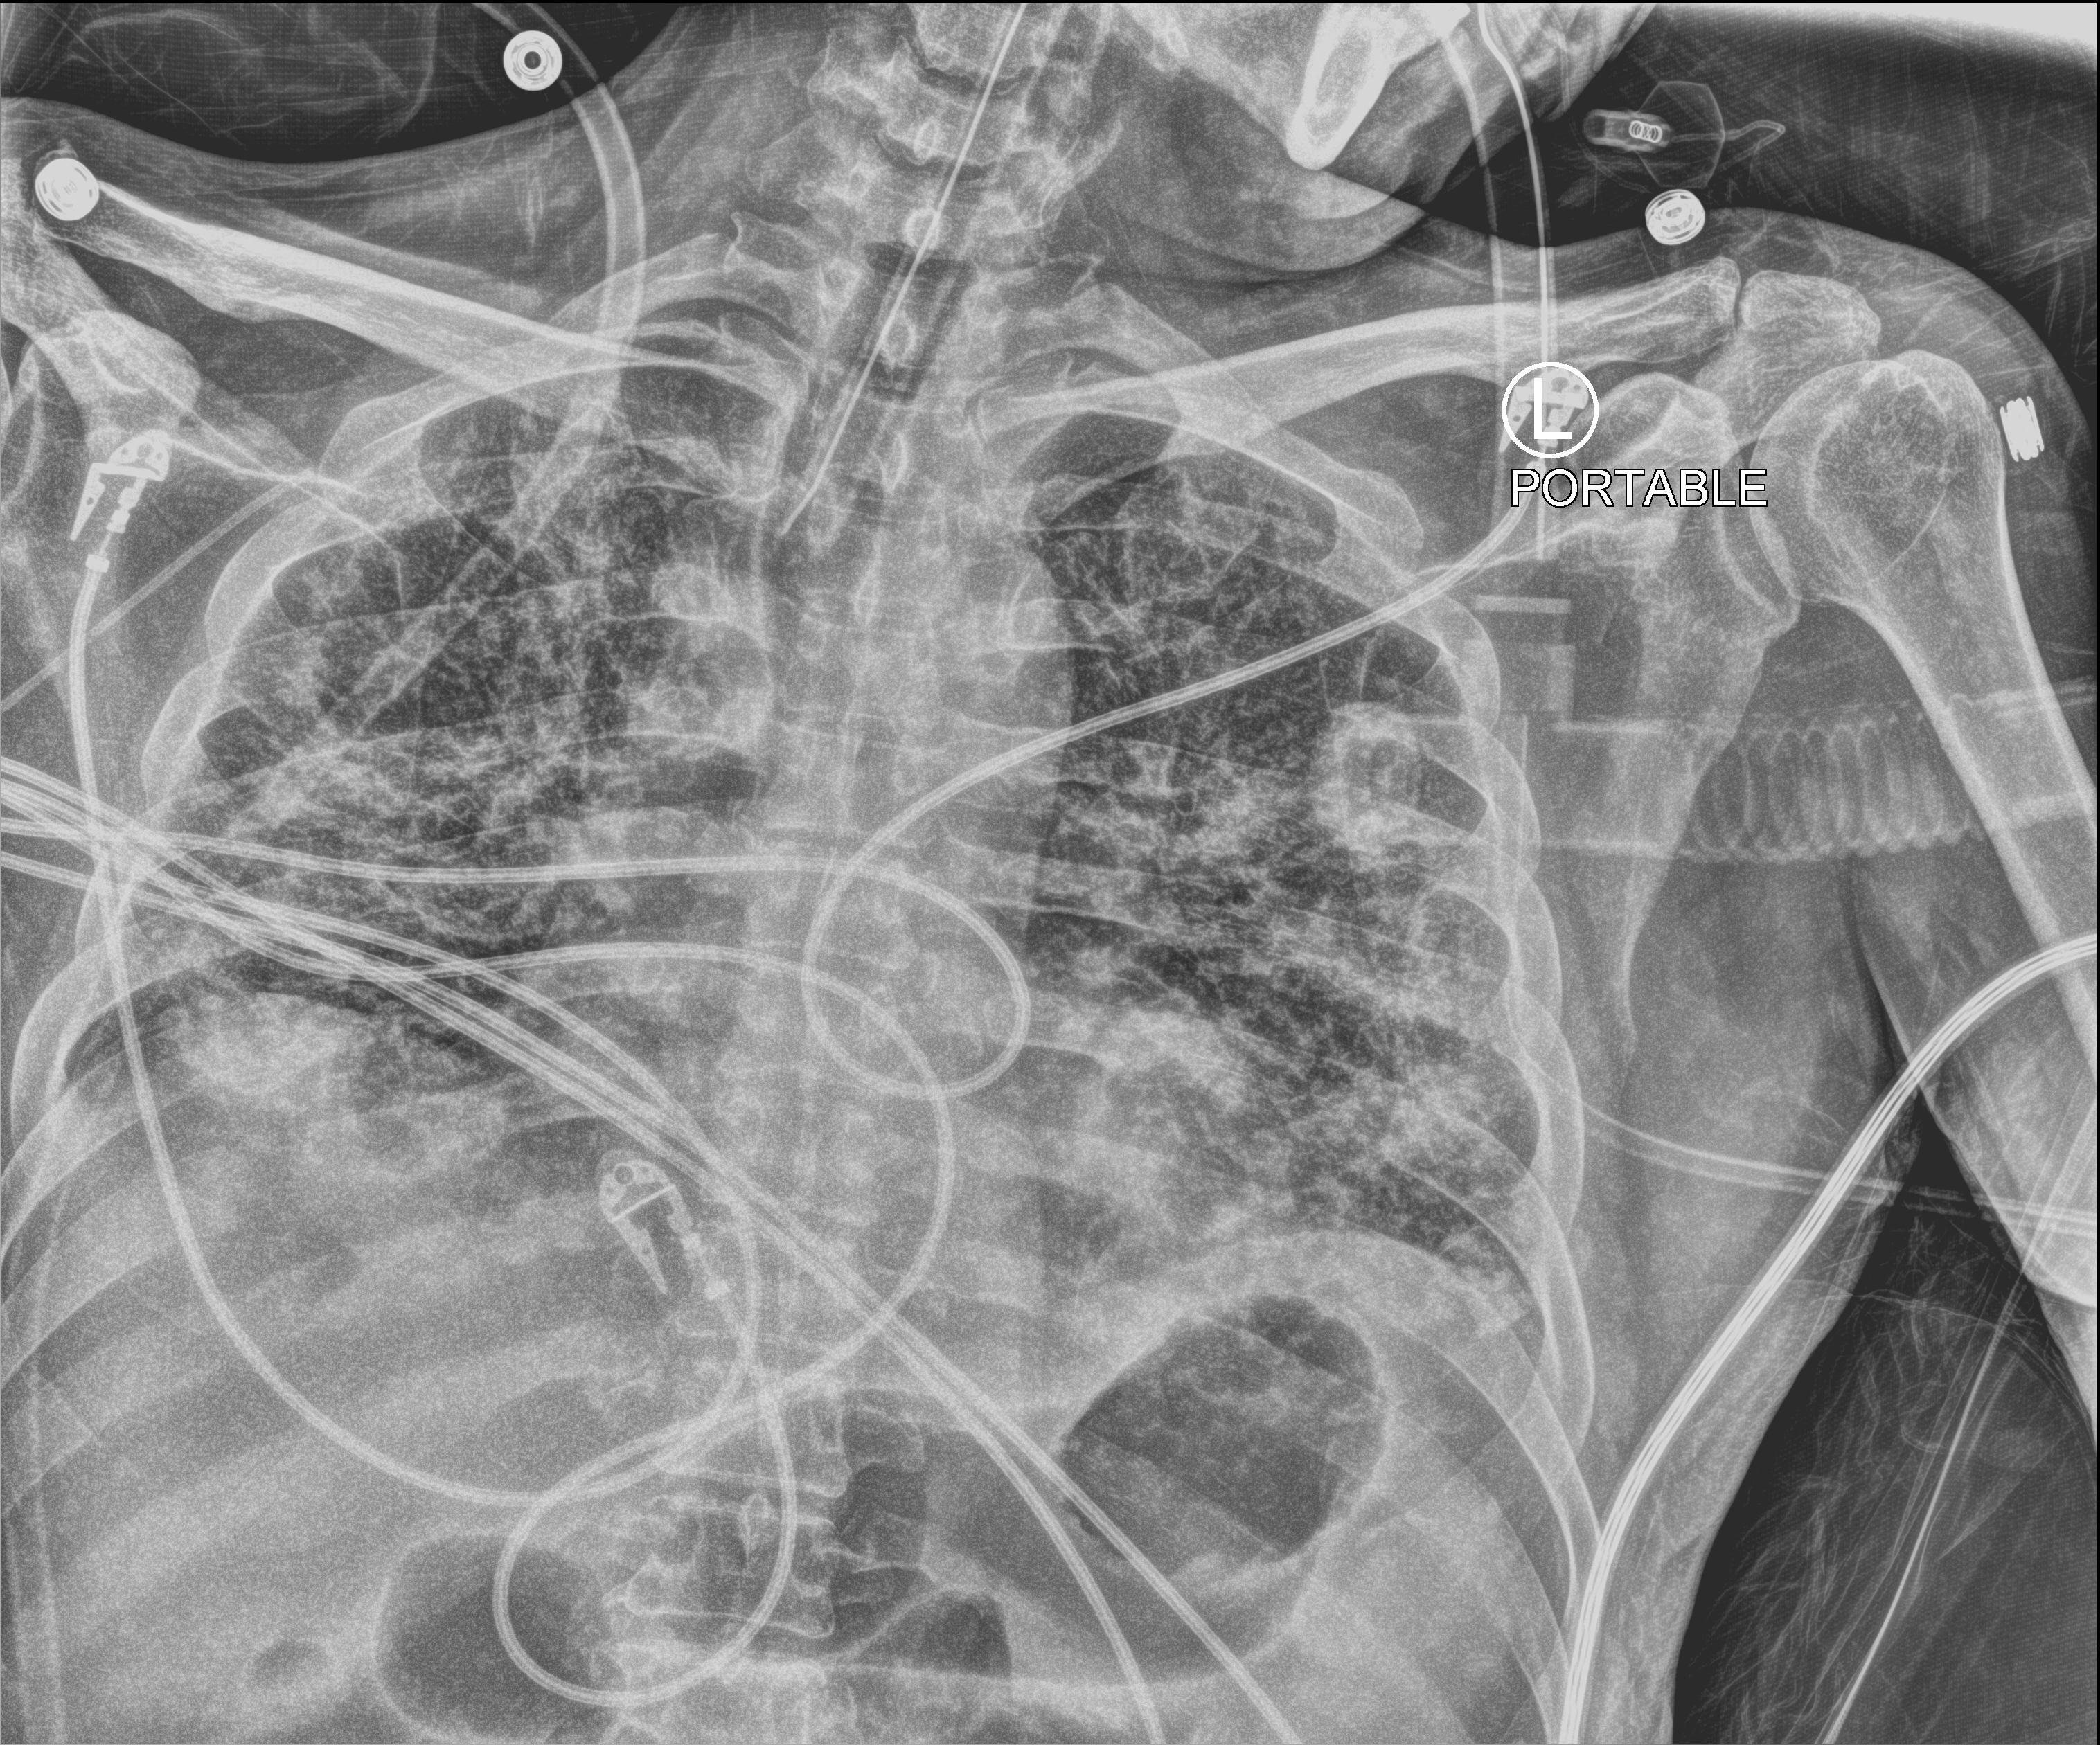
Chest X-ray (portable); anteroposterior (AP) projection. Male patient hospitalised with COVID-19, age 18–59 years.
Hospital-stay facts (about this admission, not read from this image; timing relative to this image not recorded):
- diabetes (admission record): yes
- admitted to intensive care during this hospital stay: yes